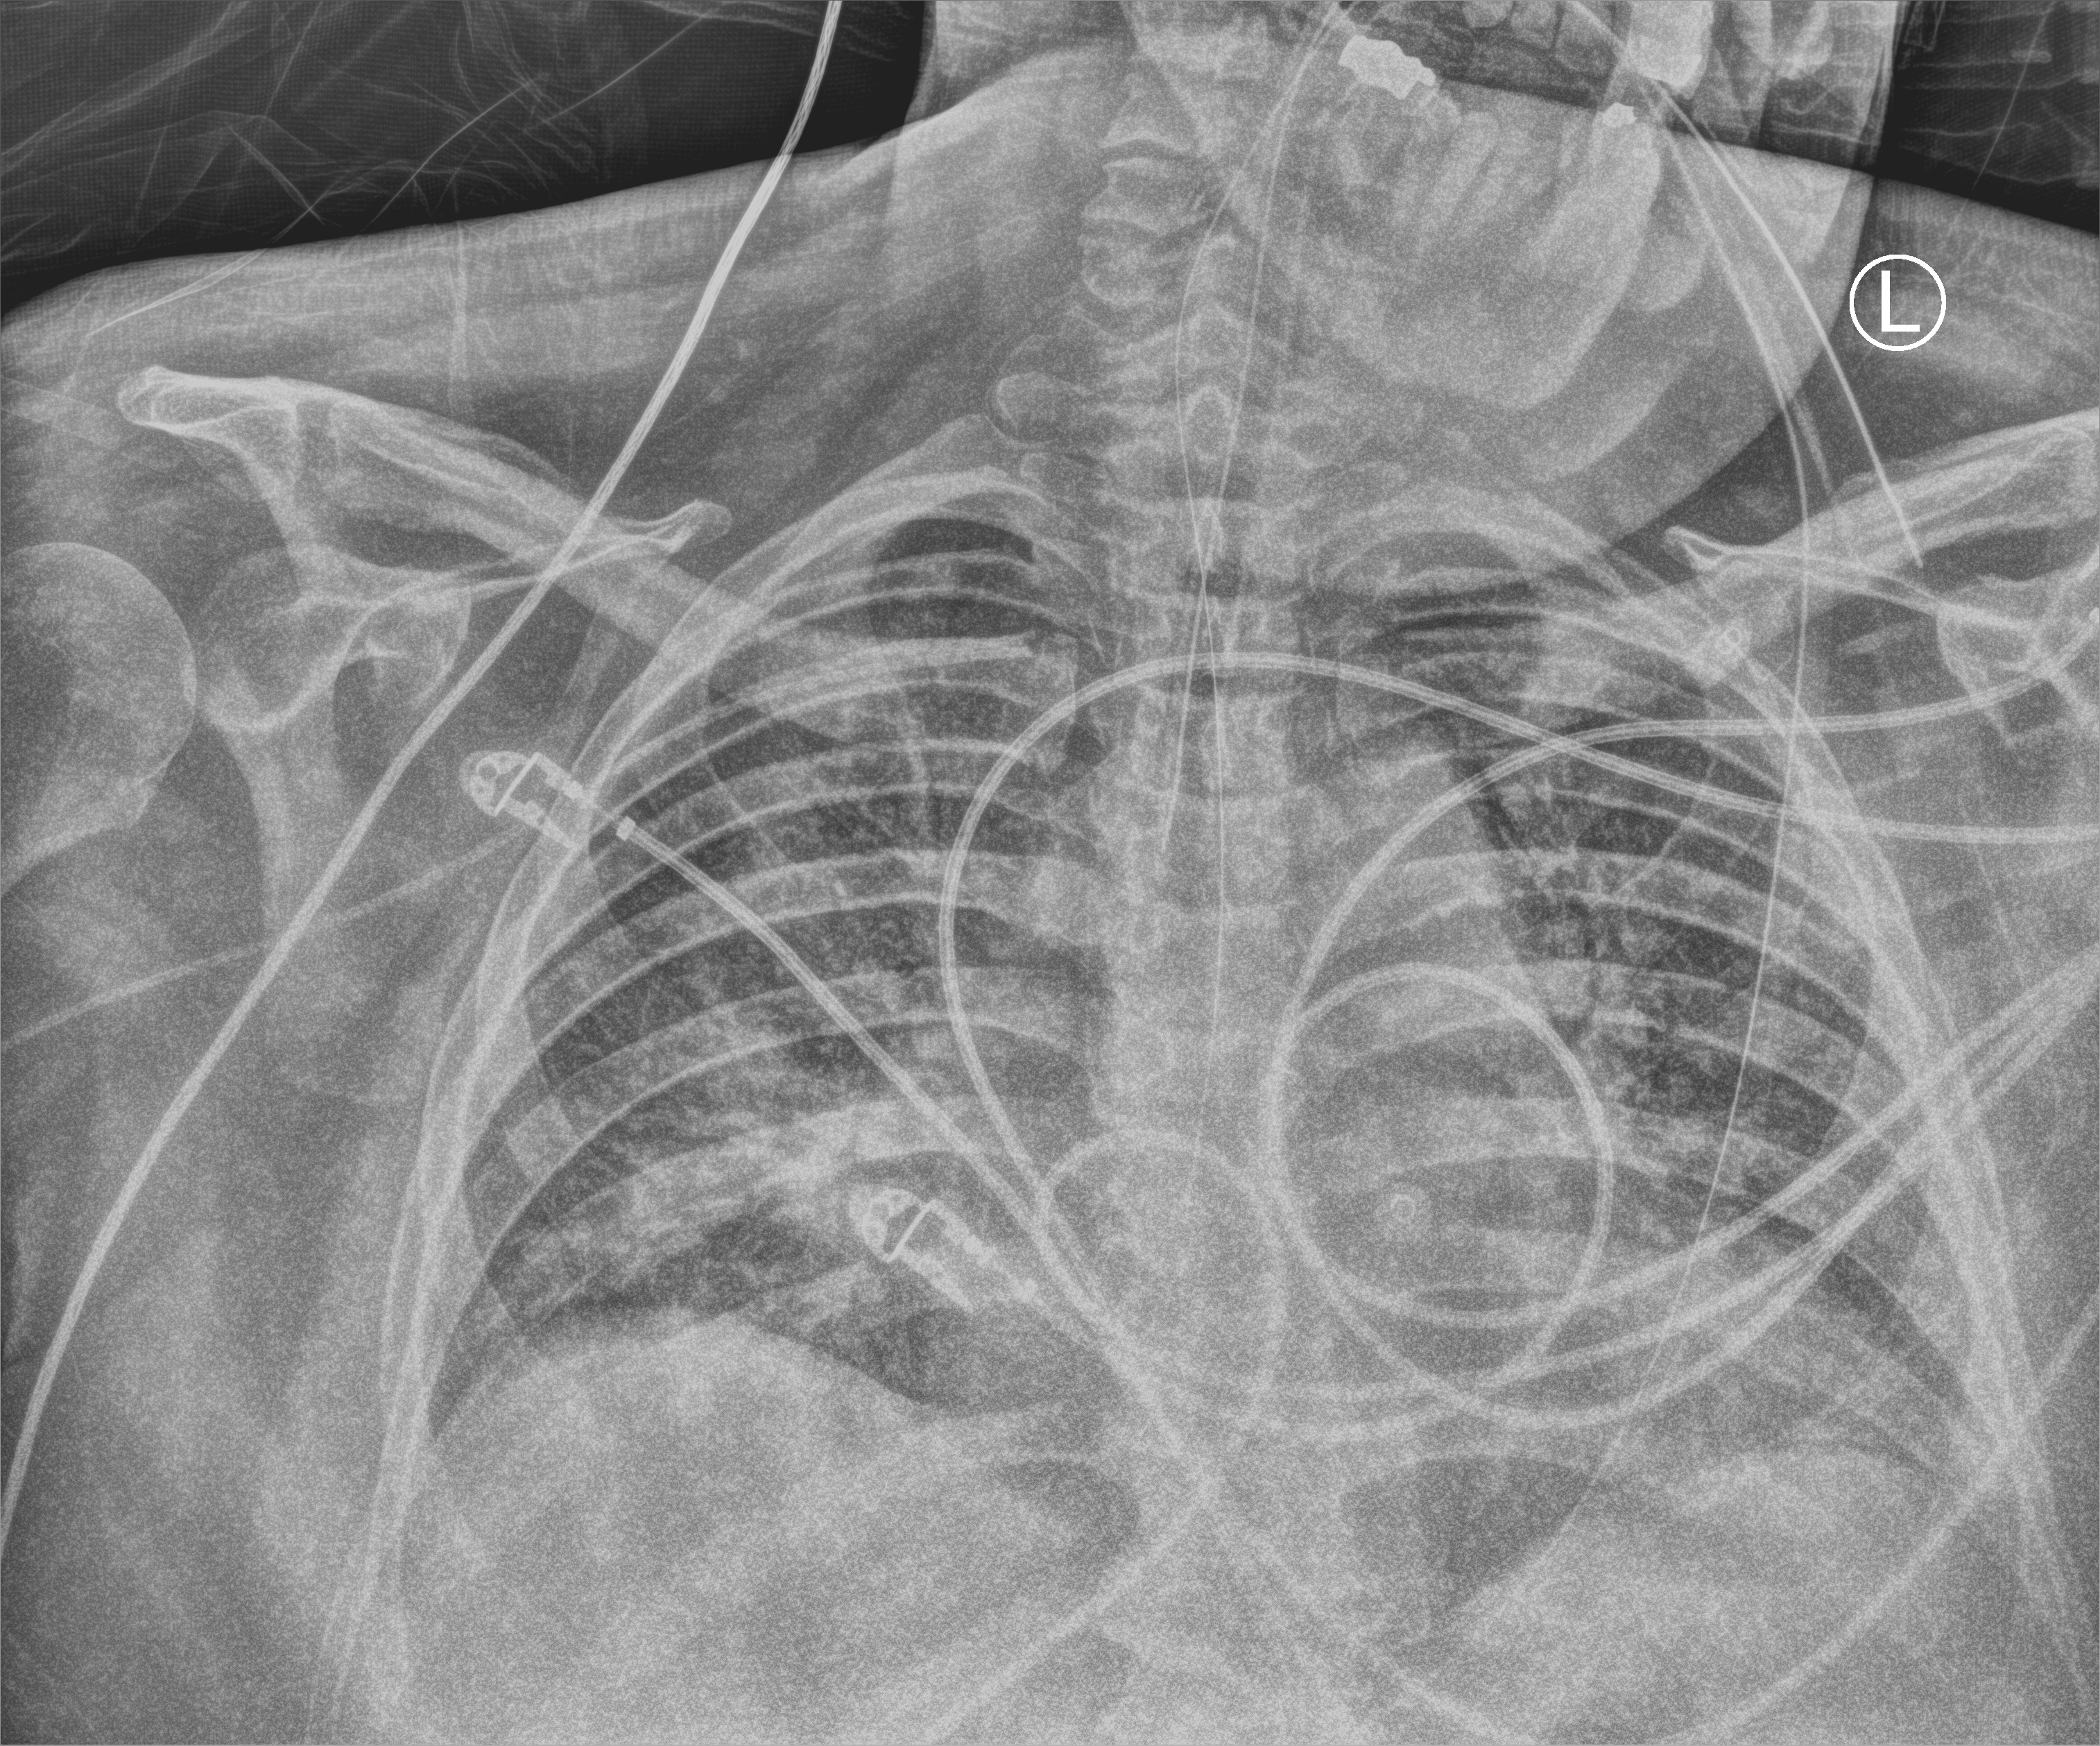
Chest X-ray (portable), anteroposterior (AP) projection. Male patient hospitalised with COVID-19, age 18–59 years.
From the hospital-stay record, not from the radiograph (when in the stay this image was taken is not recorded): admitted to intensive care during this hospital stay: yes; smoking status (admission record): never; mechanically ventilated during this hospital stay: yes.